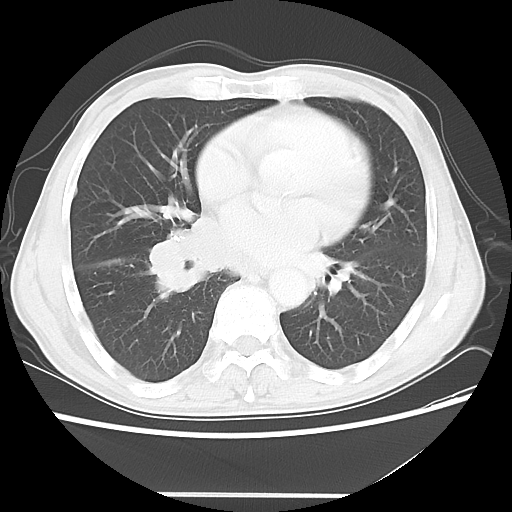
Chest CT, one axial slice; slice 24 of 56 in the series (ordered by position); reconstruction kernel LUNG; 120 kVp; lung window (W 1500 / L -600 HU); 5 mm slice thickness; 512 × 512 image matrix, field of view 344 × 344 mm. Patient: male, 65 years. Case-level facts recorded for this patient, not image findings: clinical TNM (as recorded): T1c N3 M0.
Outlined on this slice (bounding box drawn by a radiologist):
- lung tumour (recorded histology: small cell carcinoma): box from (x=148, y=212) to (x=269, y=298) px